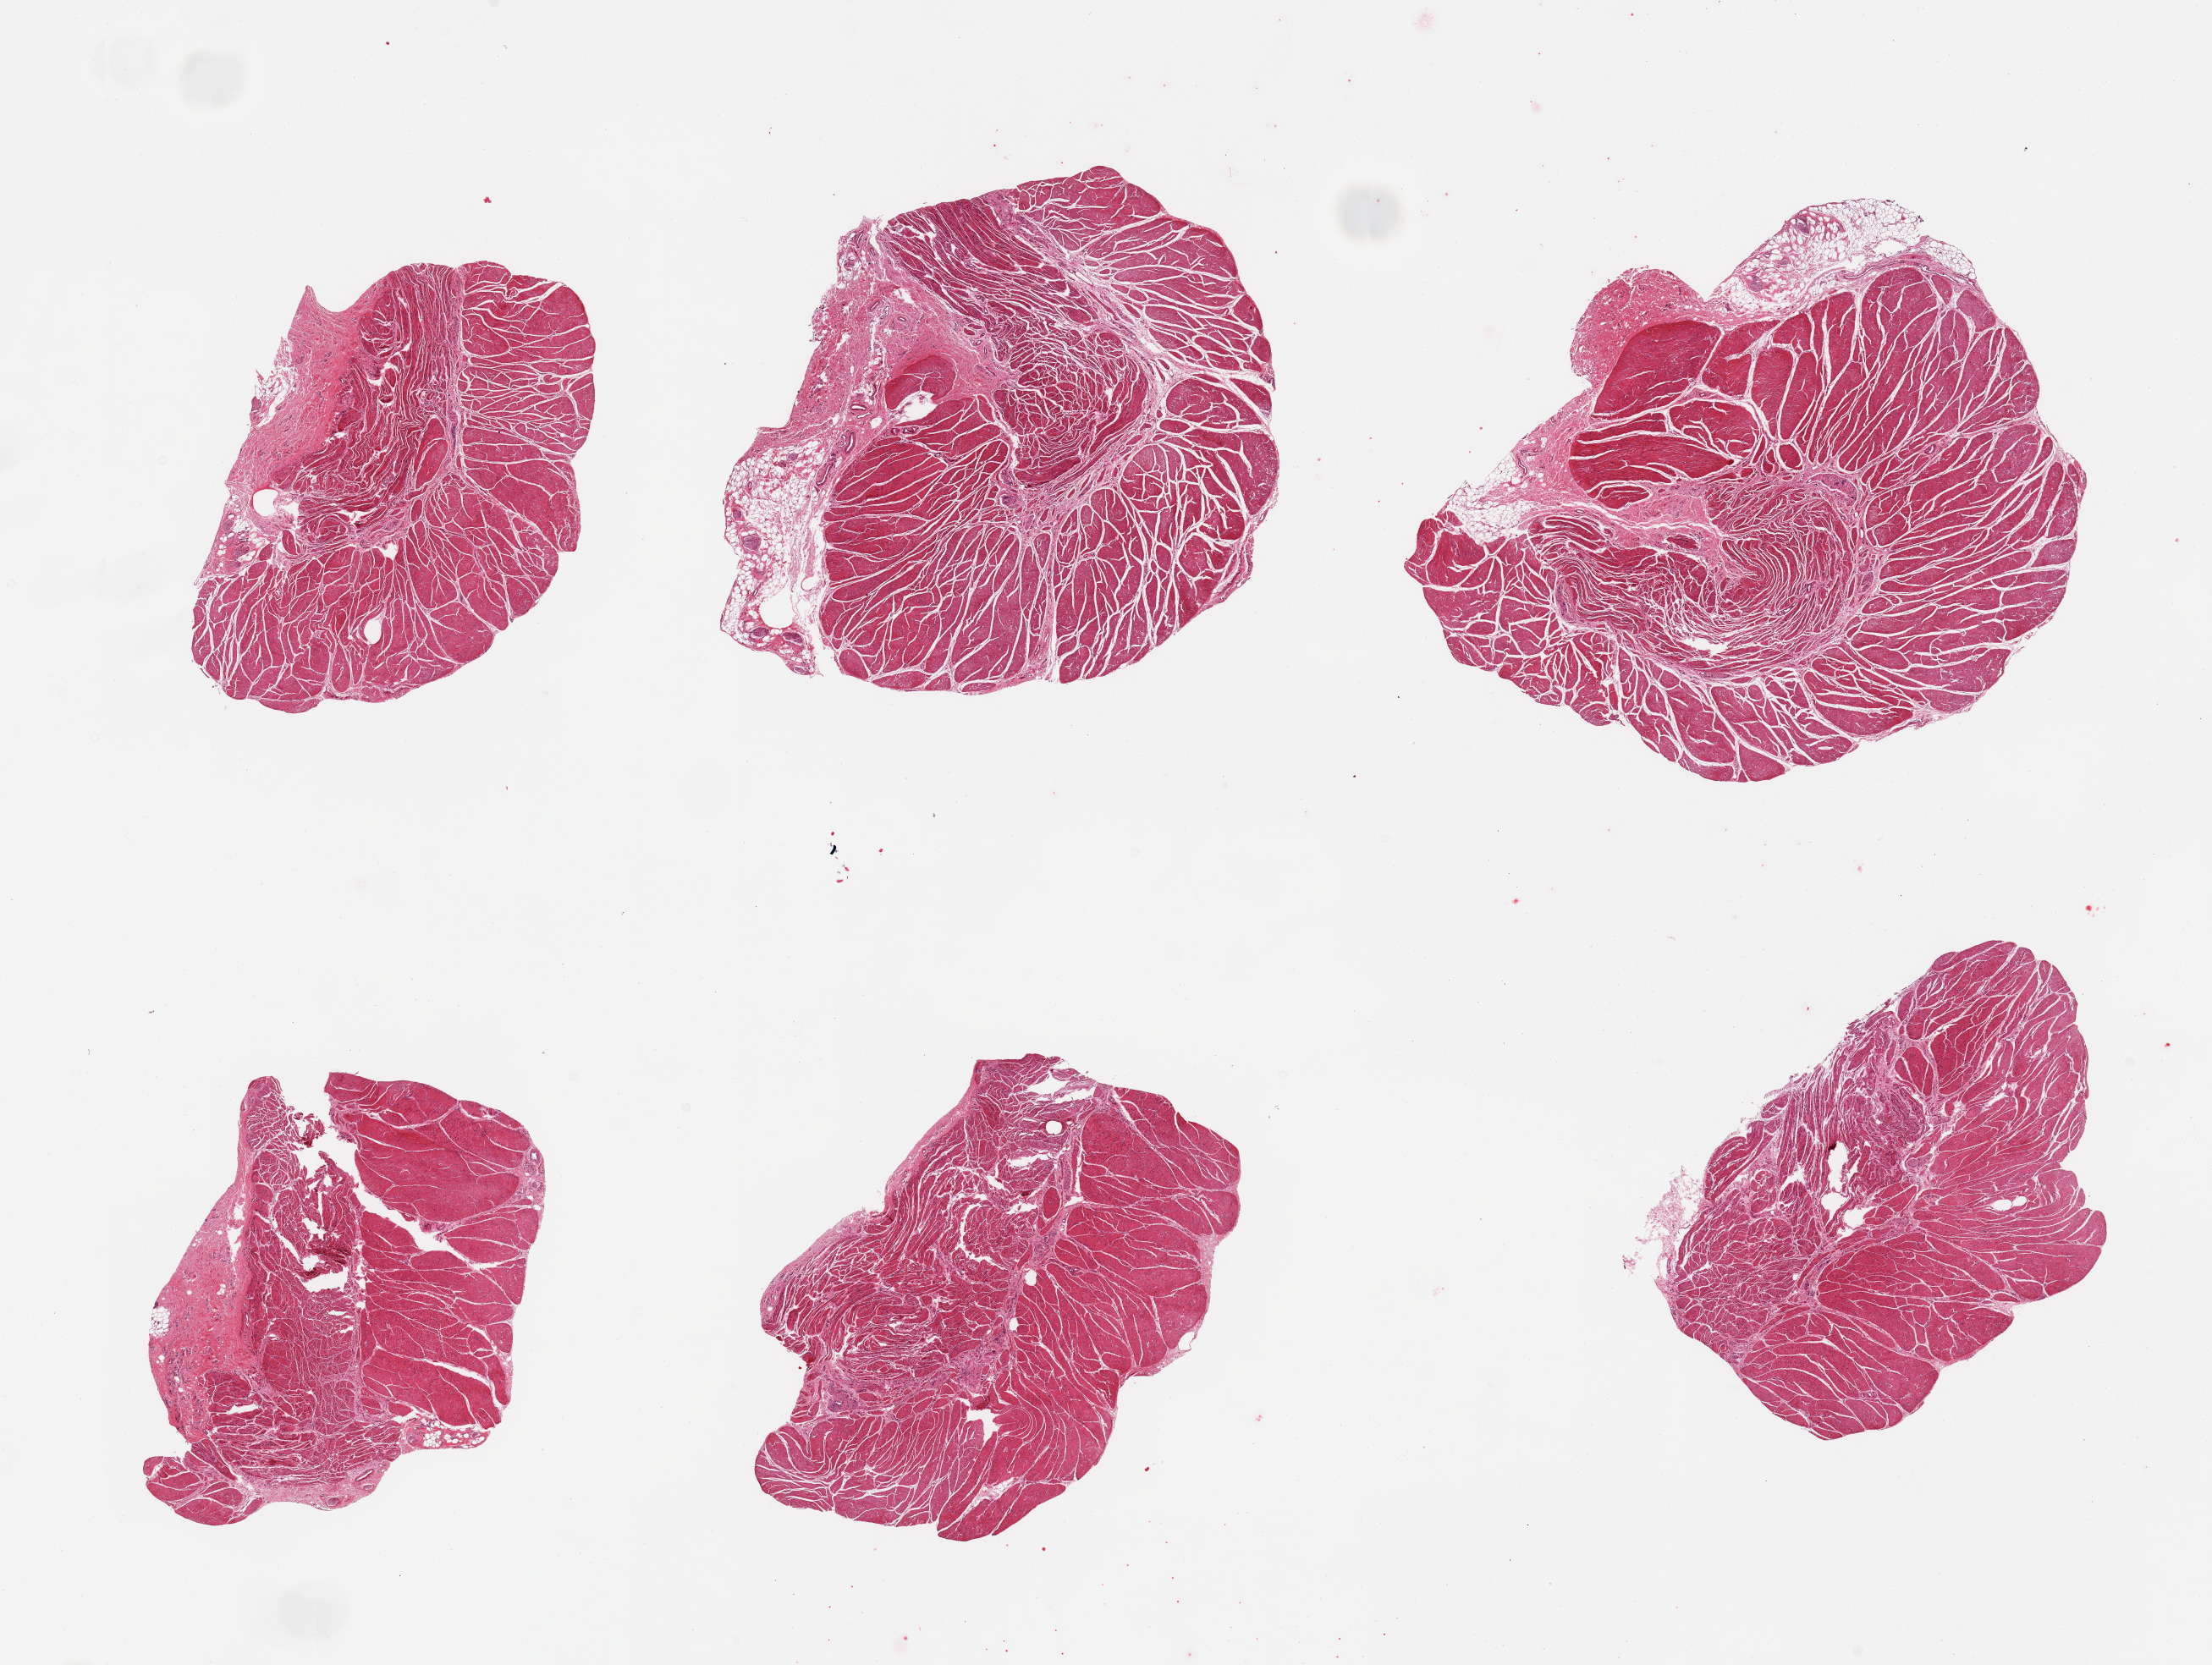
Whole-slide image, haematoxylin and eosin stain, brightfield, whole scanned area (about 20.7 x 15.6 mm) shown as a low-resolution overview; PAXgene-fixed paraffin-embedded (PFPE) section; section of esophageal muscle (target tissue); tissue donor sample. Donor: male.
• pathologist's review note for this sample: 6 pieces, confirmed target muscularis